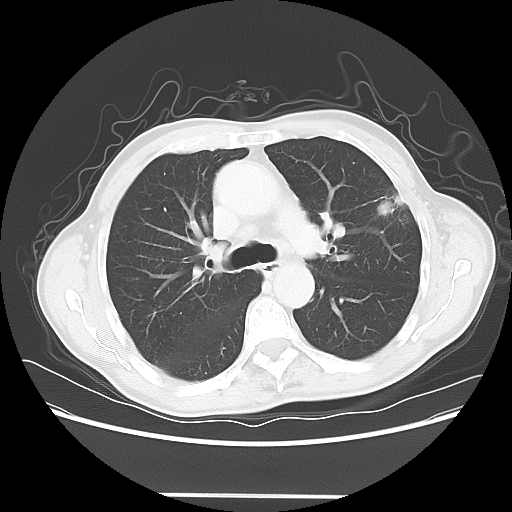
Chest CT, one axial slice; position 41 of 64 along the scan axis; reconstruction kernel LUNG; lung window (W 1500 / L -600 HU); 5 mm slice thickness; 512 × 512 image matrix, field of view 392 × 392 mm. Patient: male, 71 years. Case-level facts recorded for this patient, not image findings: clinical TNM (as recorded): T1c N0 M0.
Annotated regions visible in this slice (rectangle marked by the reading radiologist):
- lung tumour (recorded histology: adenocarcinoma): box from (x=369, y=186) to (x=411, y=221) px